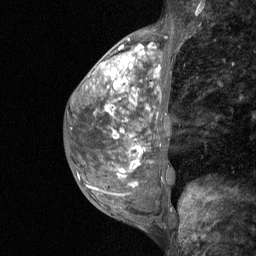
Breast MRI (dynamic contrast-enhanced), one sagittal slice. Slice 25 of 64 in the series (ordered by position). Dynamic contrast-enhanced study with each time point stored as its own series, time point 2 of 3 at this slice position (early post-contrast, ordered by acquisition time). 1.5 T. TE 4.8 ms, TR 27 ms. 2 mm slice thickness. 256 × 256 image matrix, field of view 200 × 200 mm. Patient: female, 36 years. From the clinical record (not read from this slice): setting: breast cancer imaged before/during neoadjuvant chemotherapy; receptor status: HR-positive, HER2-negative.
Structures marked on this image (semi-automatically segmented with operator editing):
- analysis volume of interest (the breast-tissue region the enhancement analysis was run in; not a lesion): bounding box (x1, y1, x2, y2) in pixels: (73, 56, 174, 210)
- tumour enhancement mask (voxels above the 90 % enhancement threshold inside the analysis volume of interest): (110, 57, 131, 87)